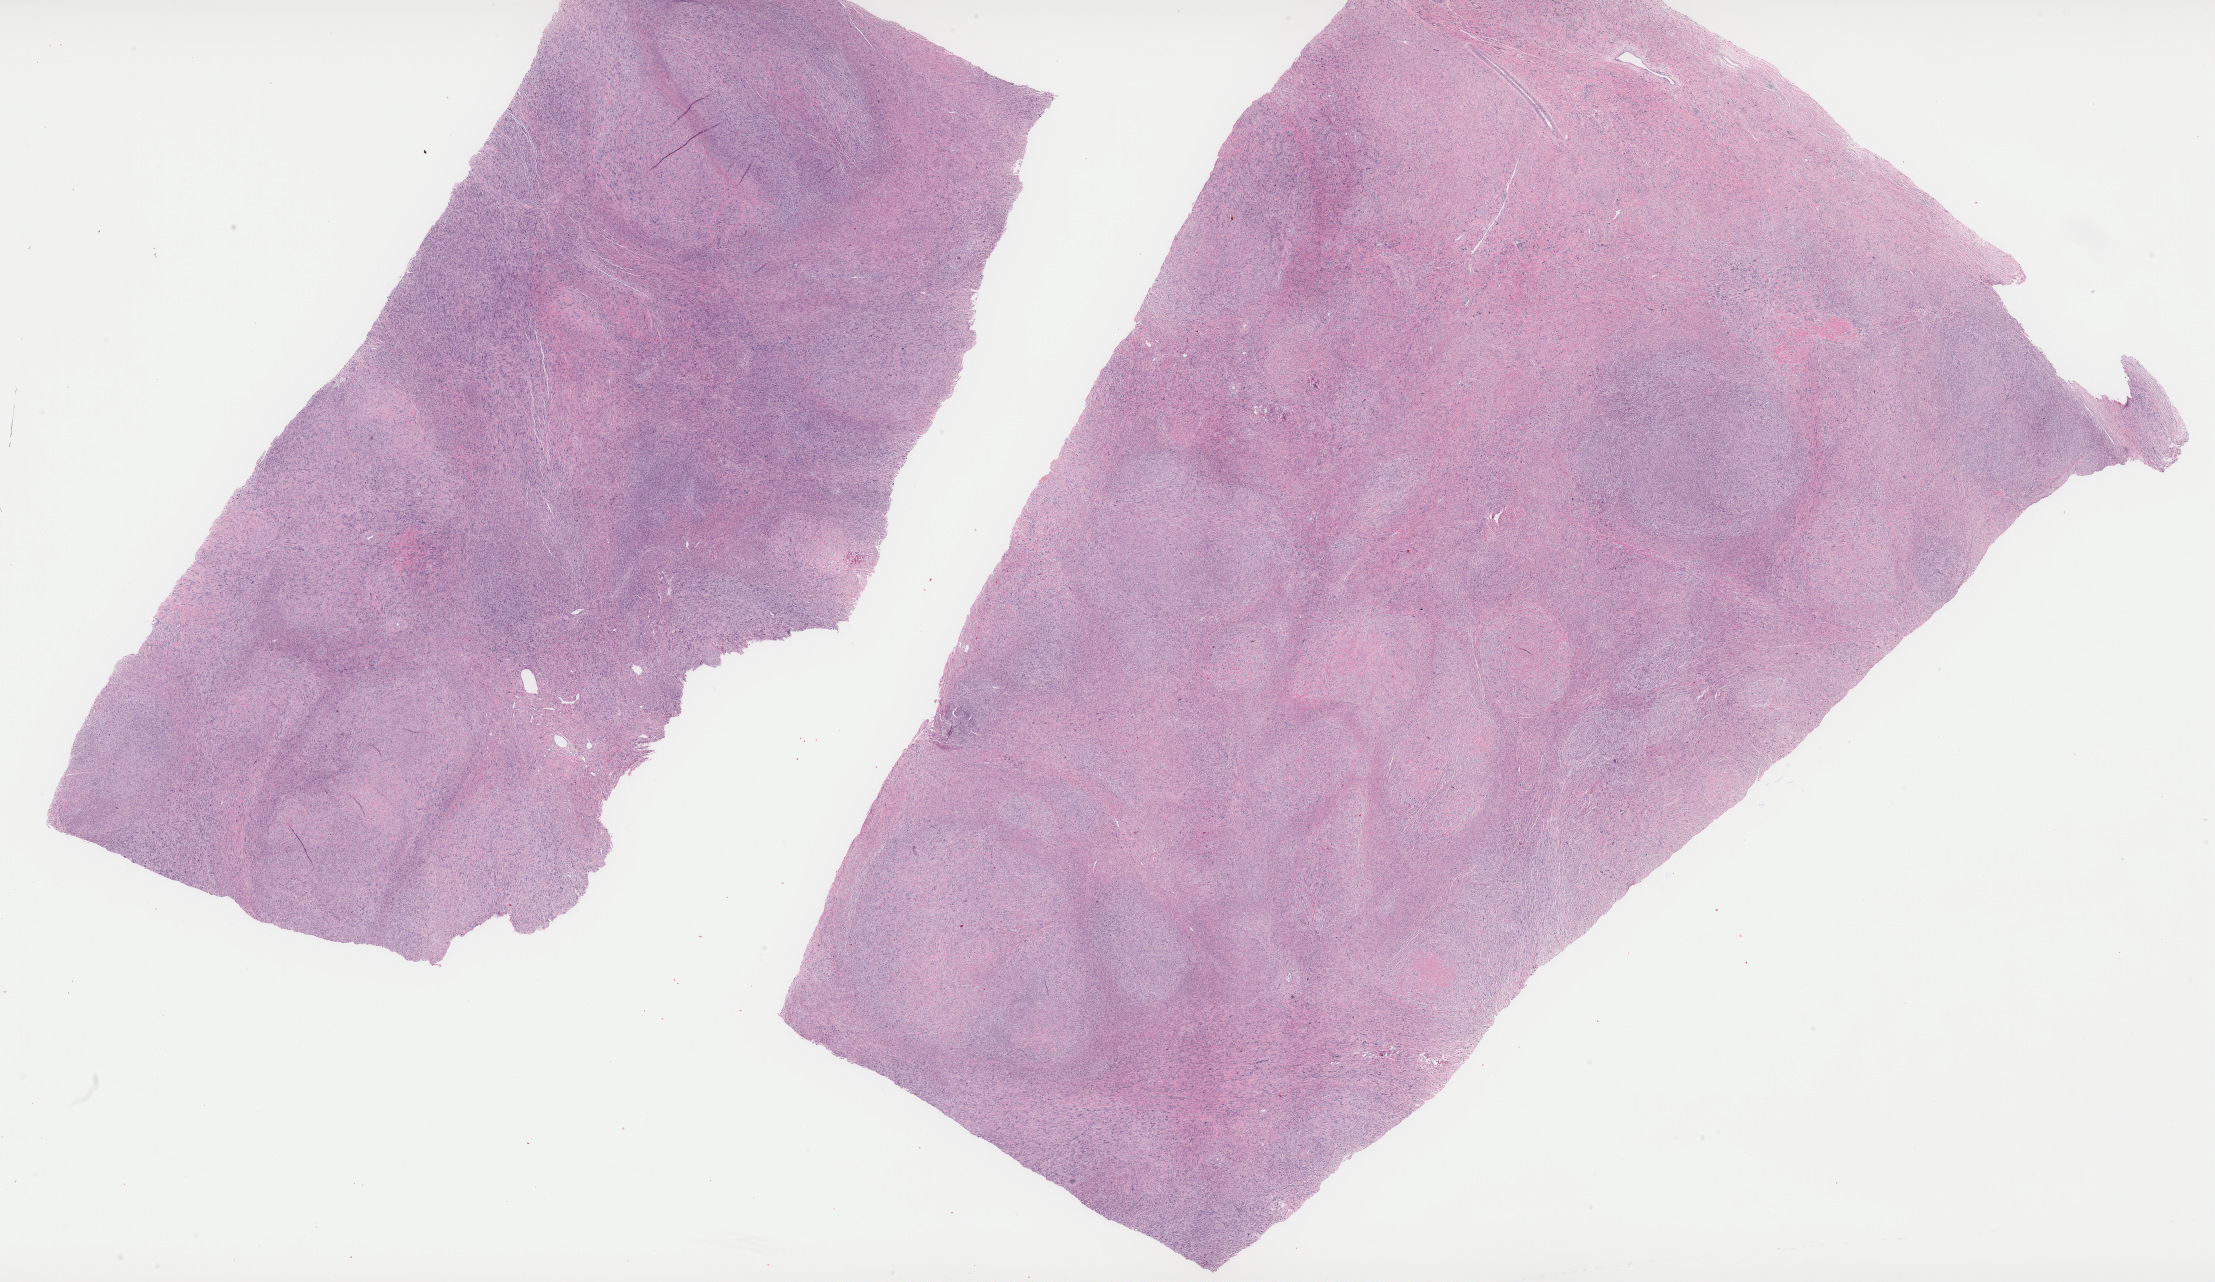
Hematoxylin and eosin (H&E) stained whole-slide image — whole scanned area (about 35.4 x 20.5 mm) shown as a low-resolution overview; FFPE section; sample: primary tumour, retroperitoneum and peritoneum. Male patient; age at initial diagnosis 34 years.
Diagnosis: Dedifferentiated liposarcoma (retroperitoneum).